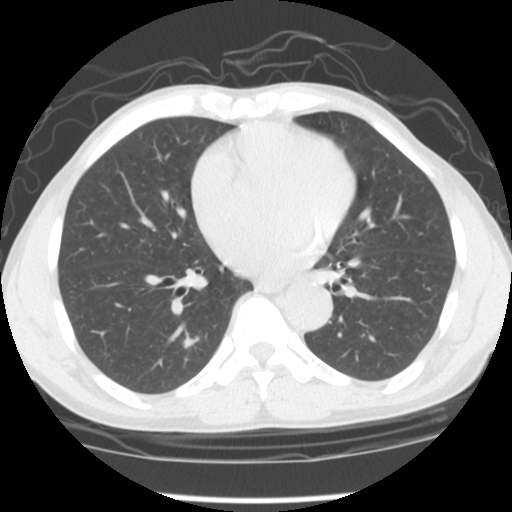
Axial slice from a low-dose chest CT screening exam, second screening round (one year after baseline), lung window (W 1500 / L -600 HU), 2.5 mm slice thickness, standard (soft-tissue) reconstruction kernel (STANDARD), slice 48 of 118 in the series. Male, age 58 years at enrolment. Current smoker at enrolment.
Expert-annotated lung lesion, bounding box (x1, y1, x2, y2) in pixels: (170, 327, 208, 360). The exam's reader record, not a measurement of the box and not confirmed to be the same lesion: non-calcified nodule or mass ≥4 mm, left upper lobe, 10 × 10 mm, poorly defined margins, ground glass attenuation, pre-existing on the prior screen: yes; interval growth: no. Note: the box lies in the patient's right hemithorax on this image, whereas the reader's record names the left lung; they may be different findings.